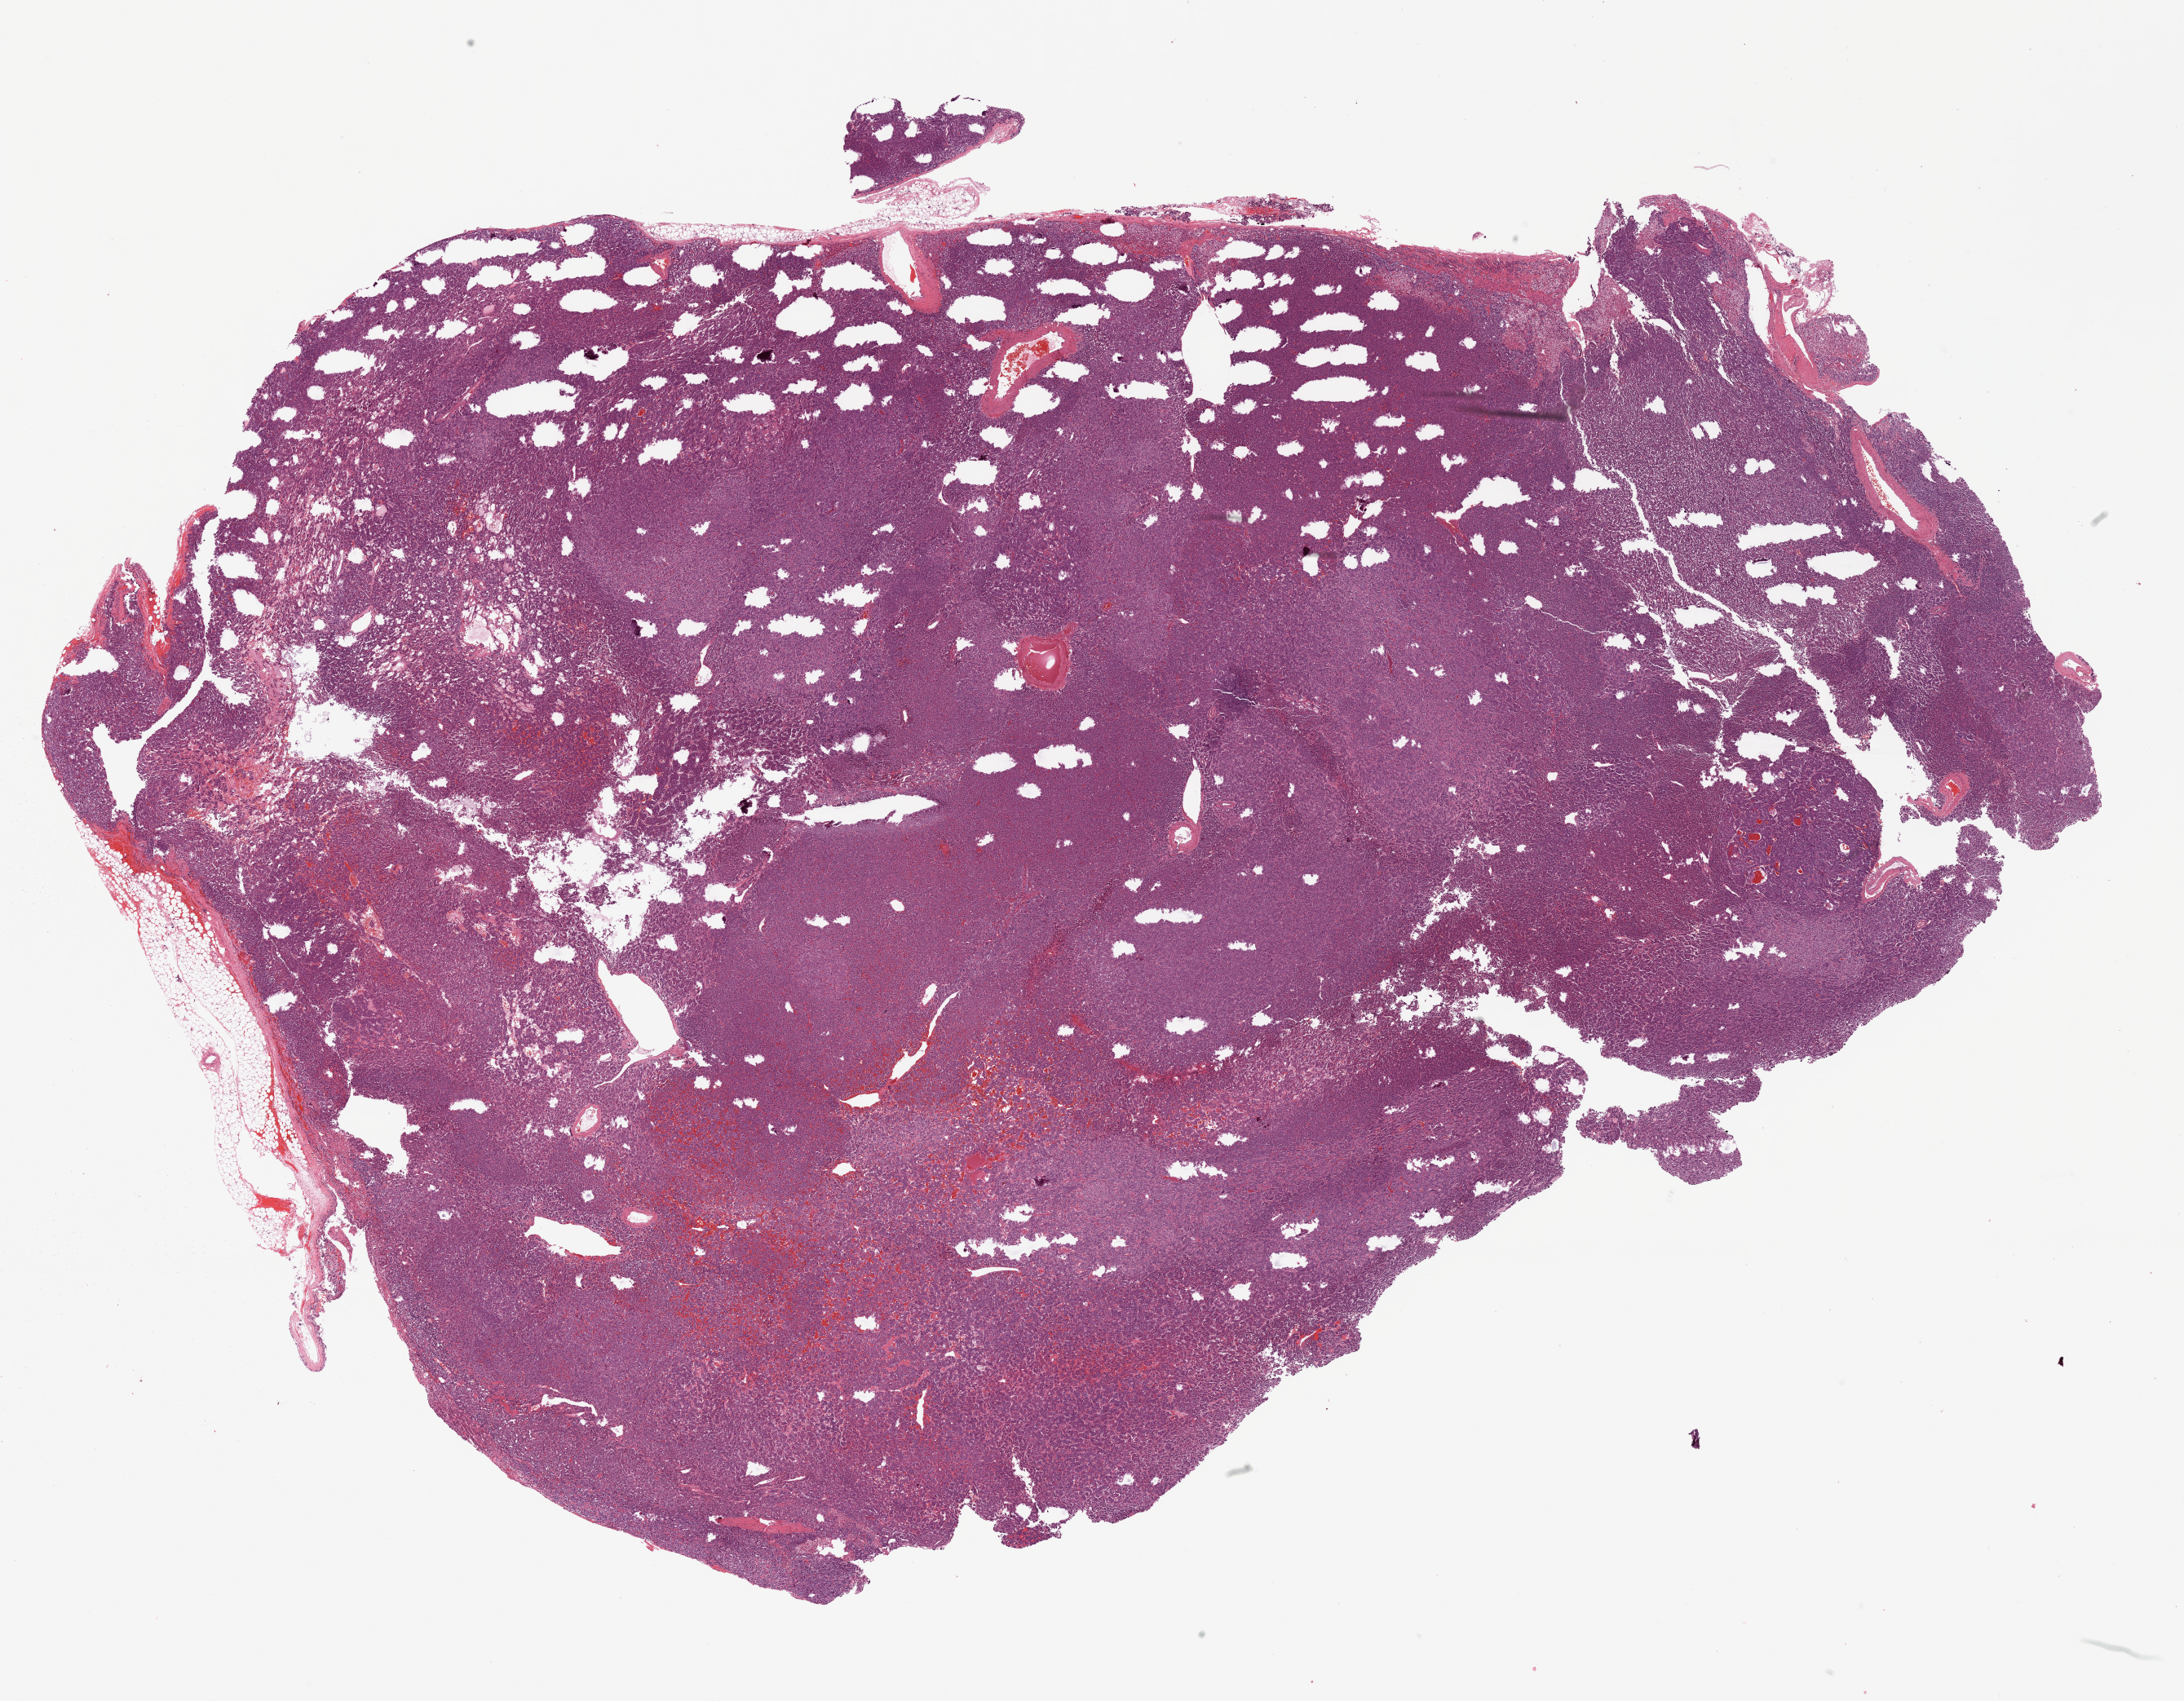
Whole-slide histology image, Hematoxylin and eosin (H&E) stained, a low-resolution overview of the entire scanned area, about 21.6 x 16.8 mm (slide scanned at 20x); formalin-fixed paraffin-embedded (FFPE) diagnostic section; adrenal gland, primary tumour sample. Patient: female, age at initial diagnosis 78 years.
Histologic diagnosis: Pheochromocytoma, malignant.